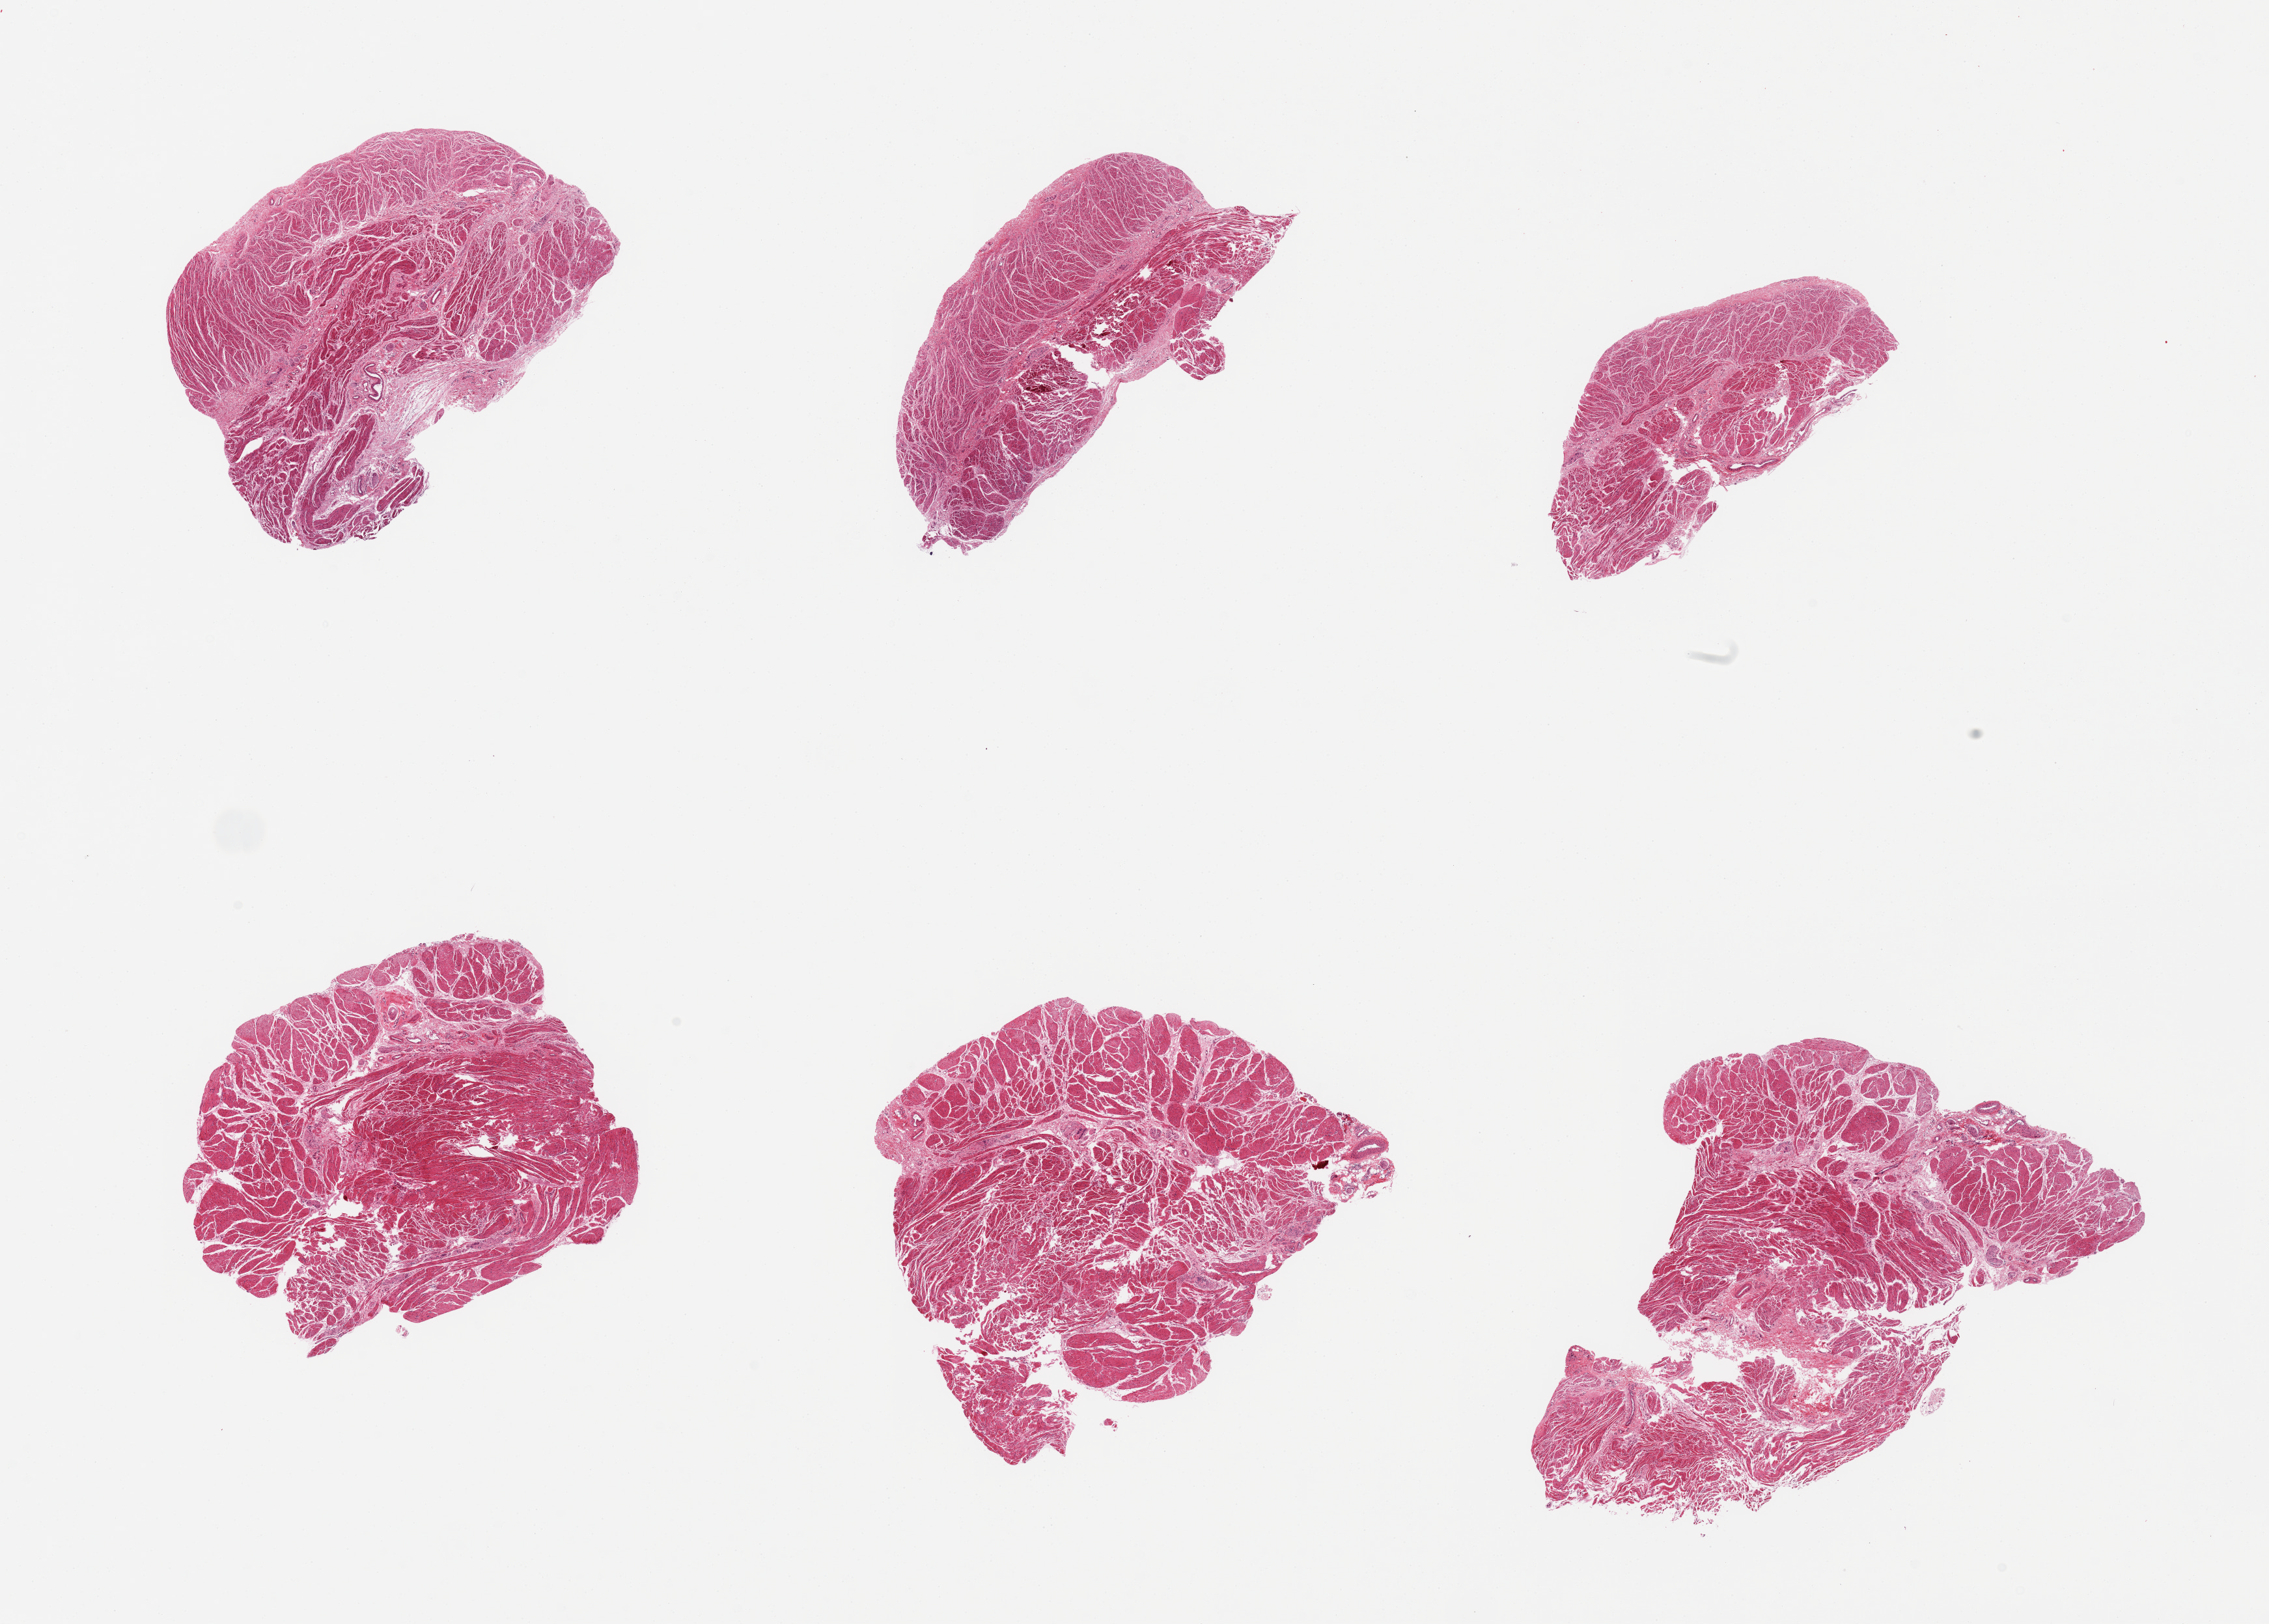
H&E whole-slide image — whole scanned area (about 27.6 x 19.7 mm, slide scanned at 20x) shown as a low-resolution overview. PAXgene-fixed, paraffin-embedded tissue. Target tissue: esophageal muscle. Donor tissue sample. Male donor.
Pathologist's review note for this sample: 6 pieces, all muscularis, no mucosa.